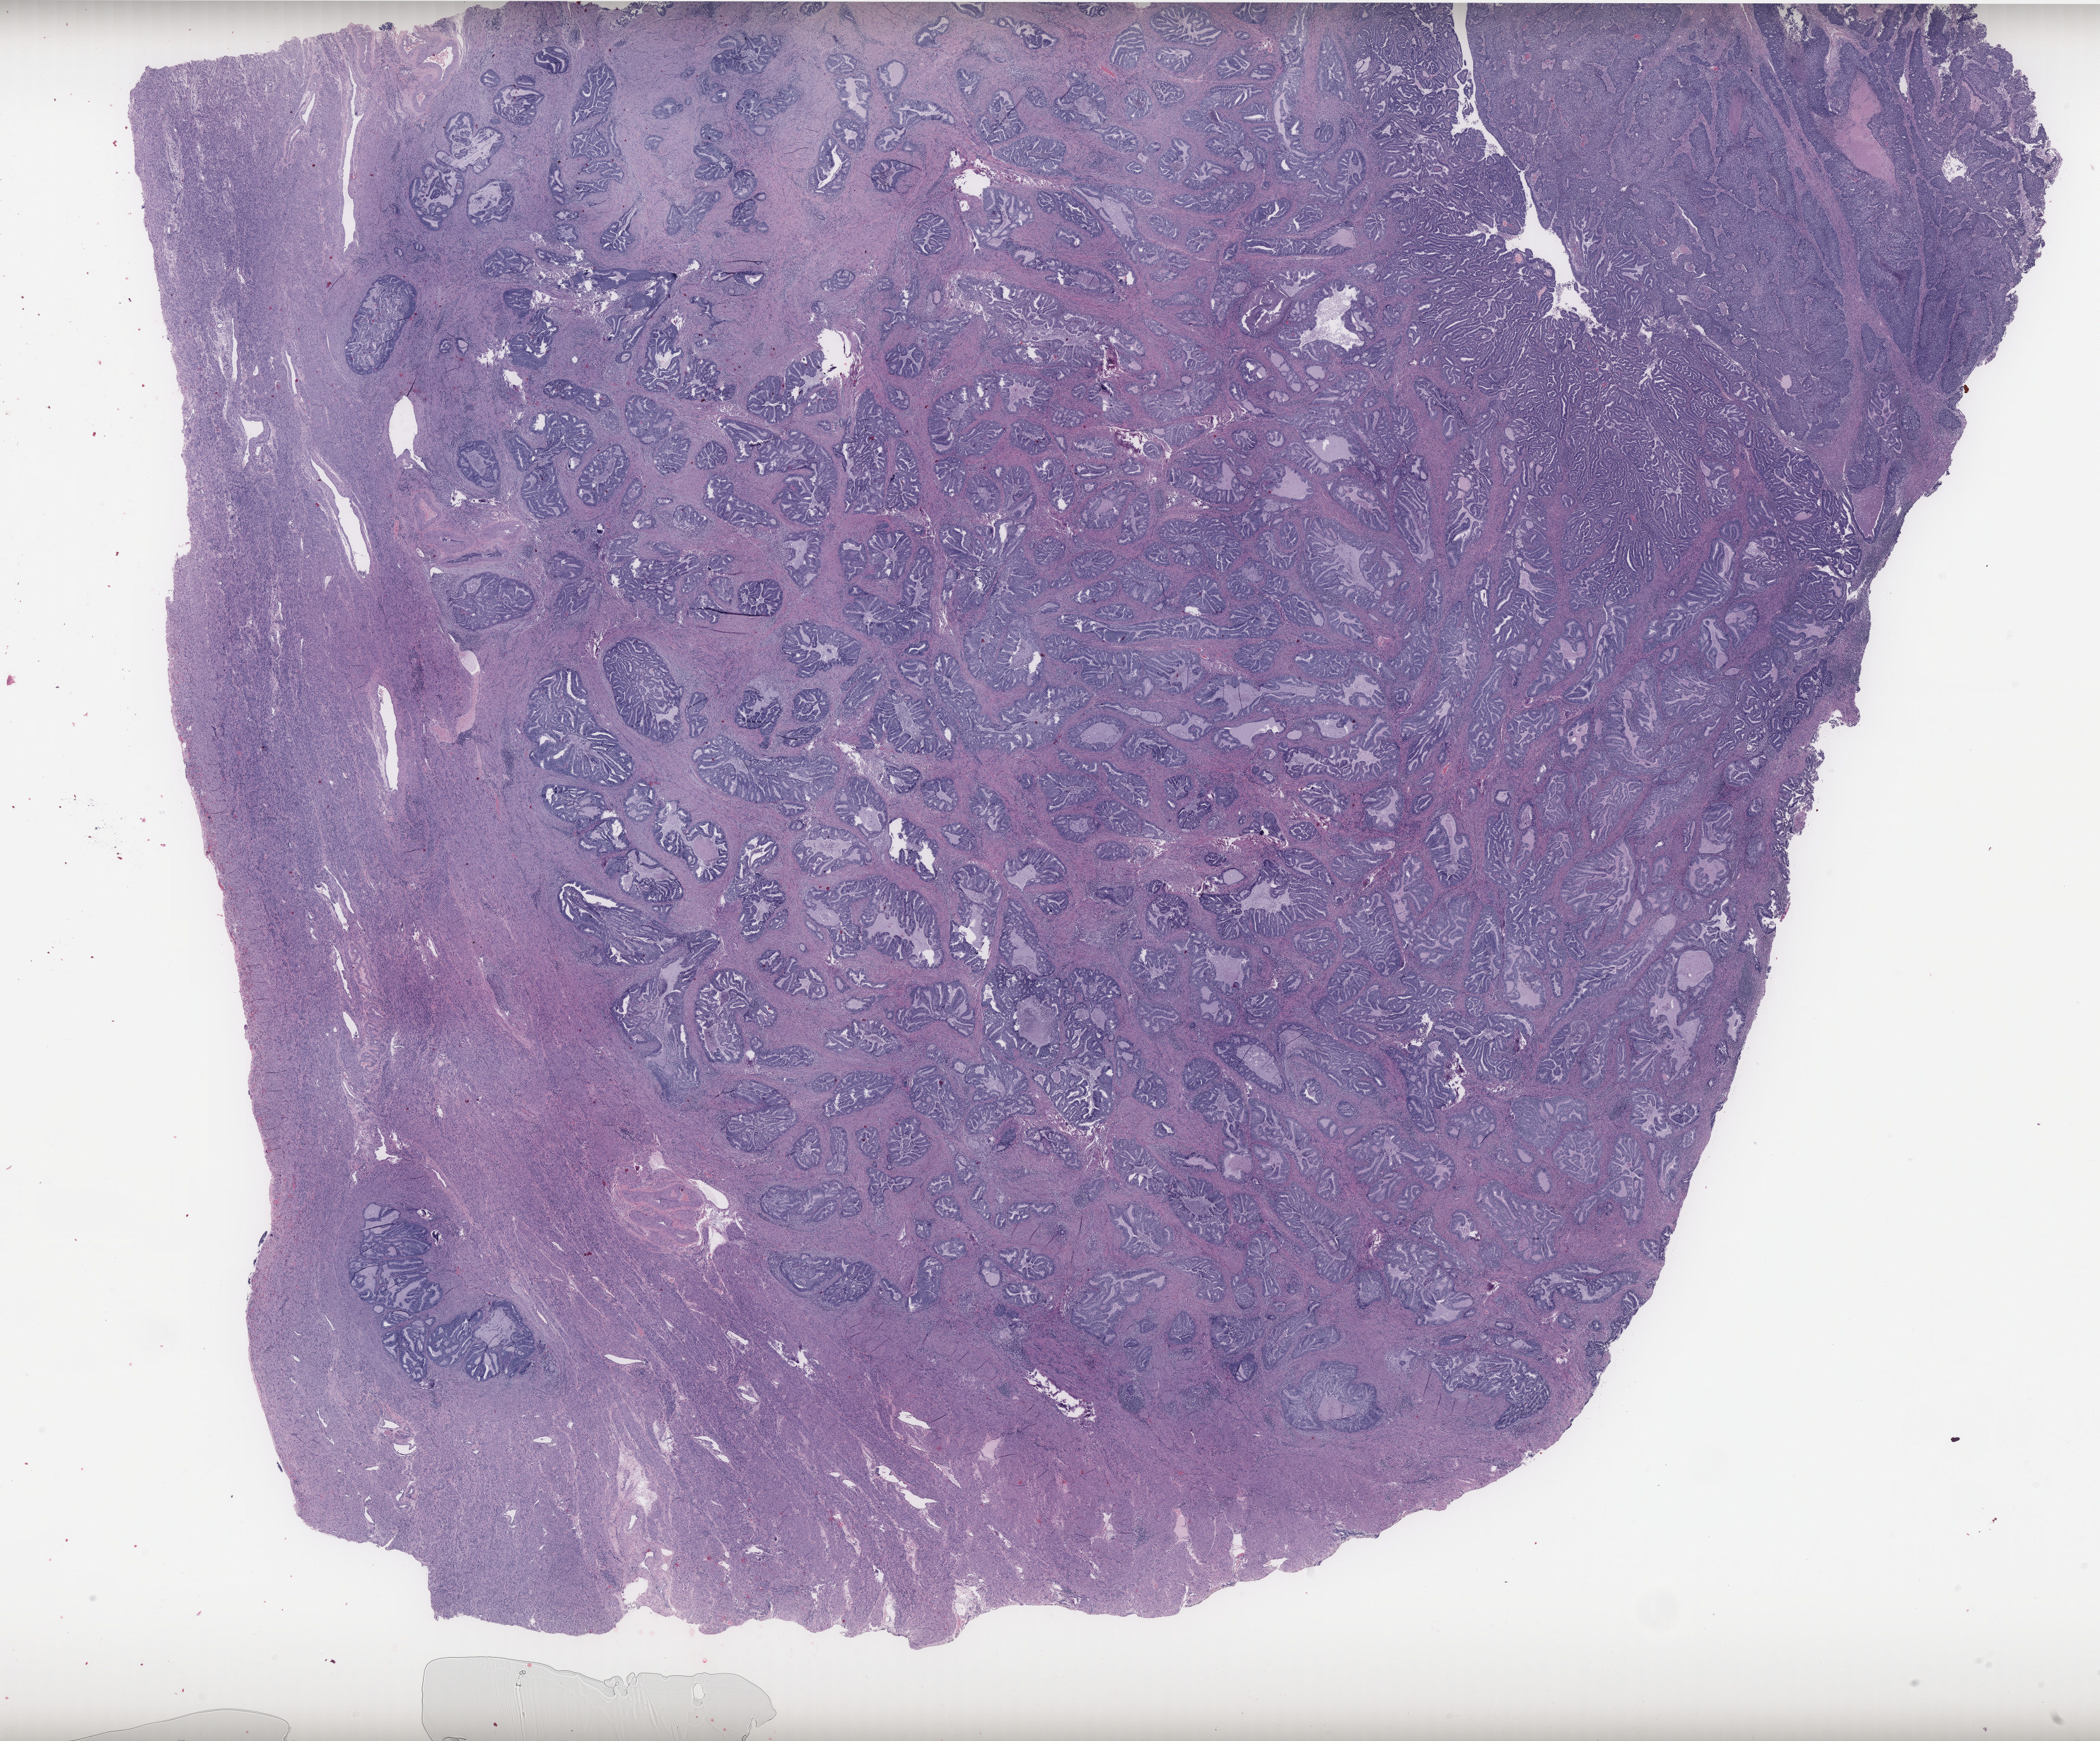
Whole-slide histology image, H&E, a low-resolution overview of the entire scanned area, about 26.7 x 22.1 mm (acquisition: 40x scan), FFPE section, sample: primary tumour, uterus. Female patient; age at initial diagnosis 57 years. Histologic grade: G2 (moderately differentiated).
FIGO stage: IB. Diagnosis: Endometrioid adenocarcinoma, NOS (endometrium). Lymph nodes positive (case pathology): 0 of 7 examined.